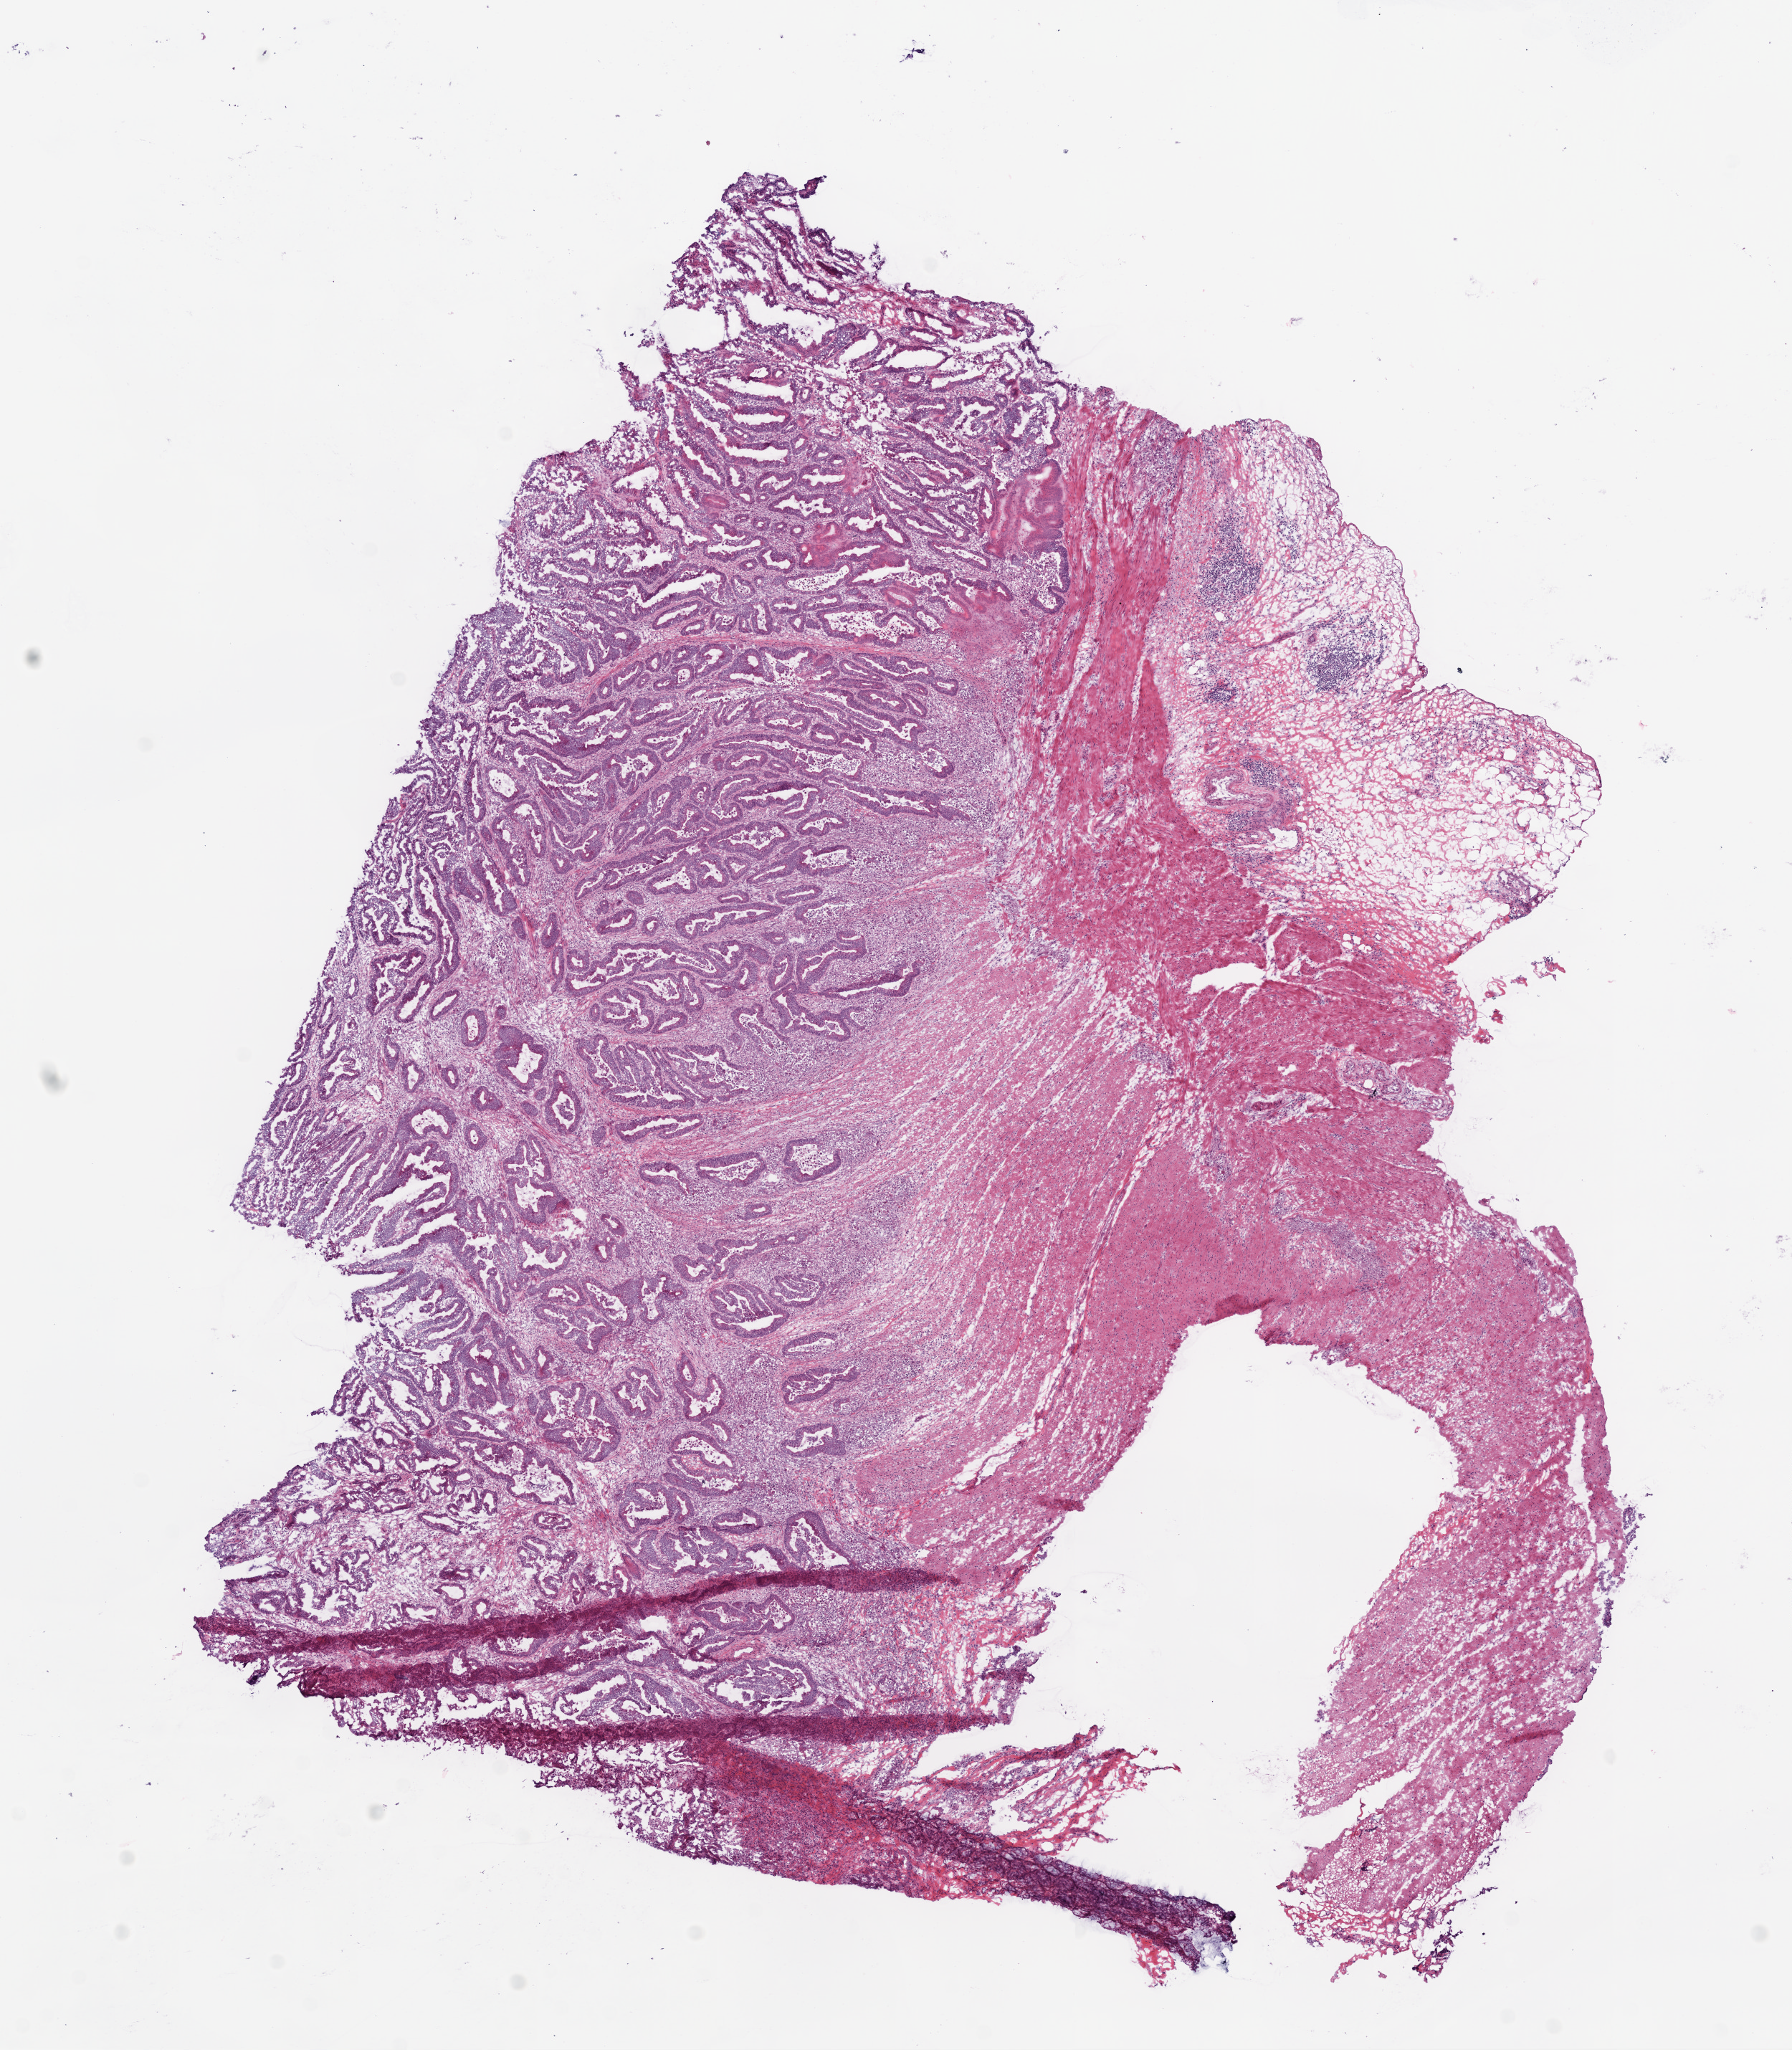
H&E whole-slide image, whole scanned area (about 10.0 x 11.5 mm, slide scanned at 20x) shown as a low-resolution overview; frozen section from the bottom of the tissue portion; primary tumour sample from the colon. Female patient; age at initial diagnosis 82 years. Composition of this section per pathologist review: tumour nuclei 75%, normal cells 20%, stromal cells 10%, necrosis 8%.
* AJCC pathologic stage: IIA (6th edition)
* lymph nodes positive (case pathology): 0 of 13 examined
* diagnosis: Adenocarcinoma, NOS